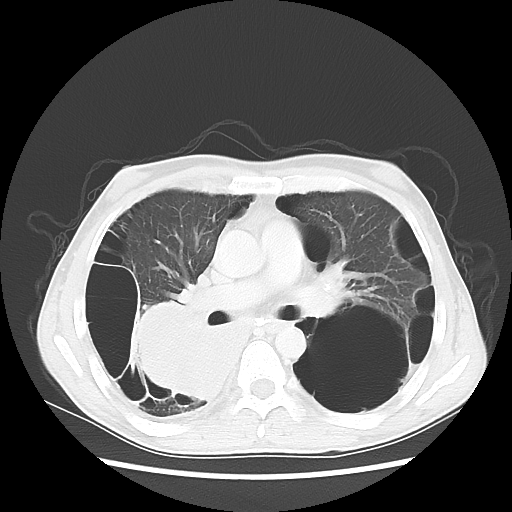
Chest CT, one axial slice; slice 32 of 57 in the series (ordered by position); 140 kVp; lung window (W 1500 / L -600 HU); 512 × 512 image matrix. Male patient, age 41 years. From the clinical record (not read from this slice): clinical TNM (as recorded): T4 N0 M1a.
Outlined on this slice (bounding box drawn by a radiologist):
- lung tumour (recorded histology: large cell carcinoma): bounding box (x1, y1, x2, y2) in pixels: (125, 301, 236, 405)